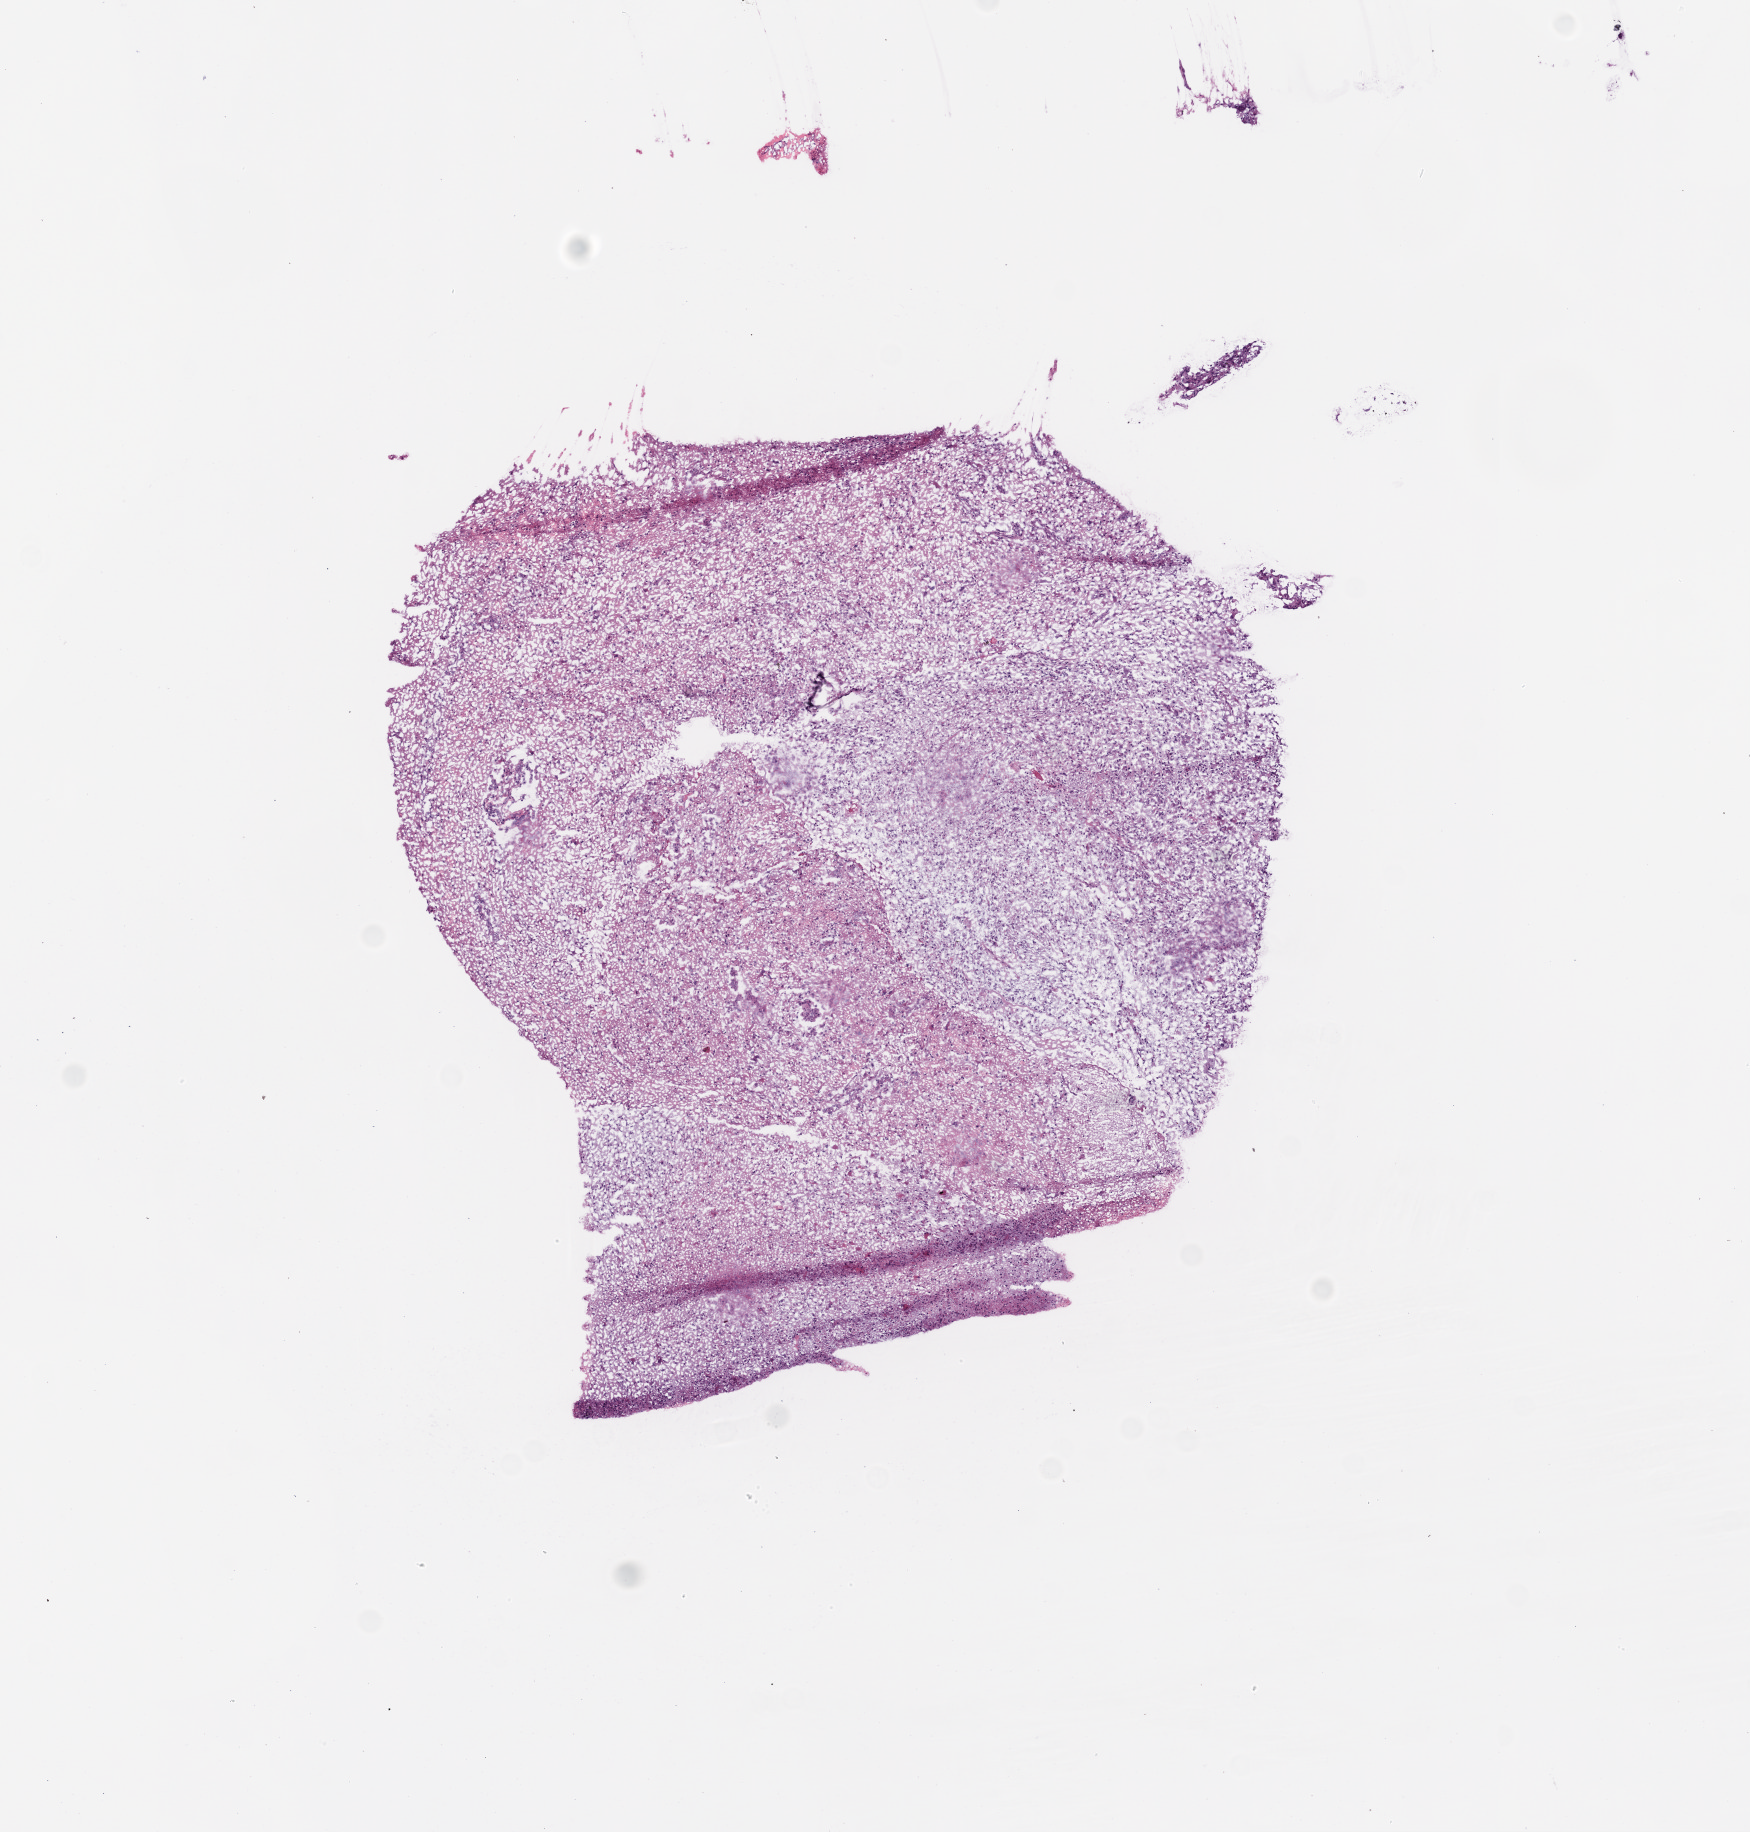
H&E whole-slide image, whole scanned area (about 7.0 x 7.3 mm) shown as a low-resolution overview; frozen section from the top of the tissue portion; primary tumour sample from the brain. Male, age 65 years at initial diagnosis. Slide review estimates, as recorded: tumour cells 97%, tumour nuclei 80%, normal cells 0%, stromal cells 0%, necrosis 3%.
- histologic diagnosis: Glioblastoma